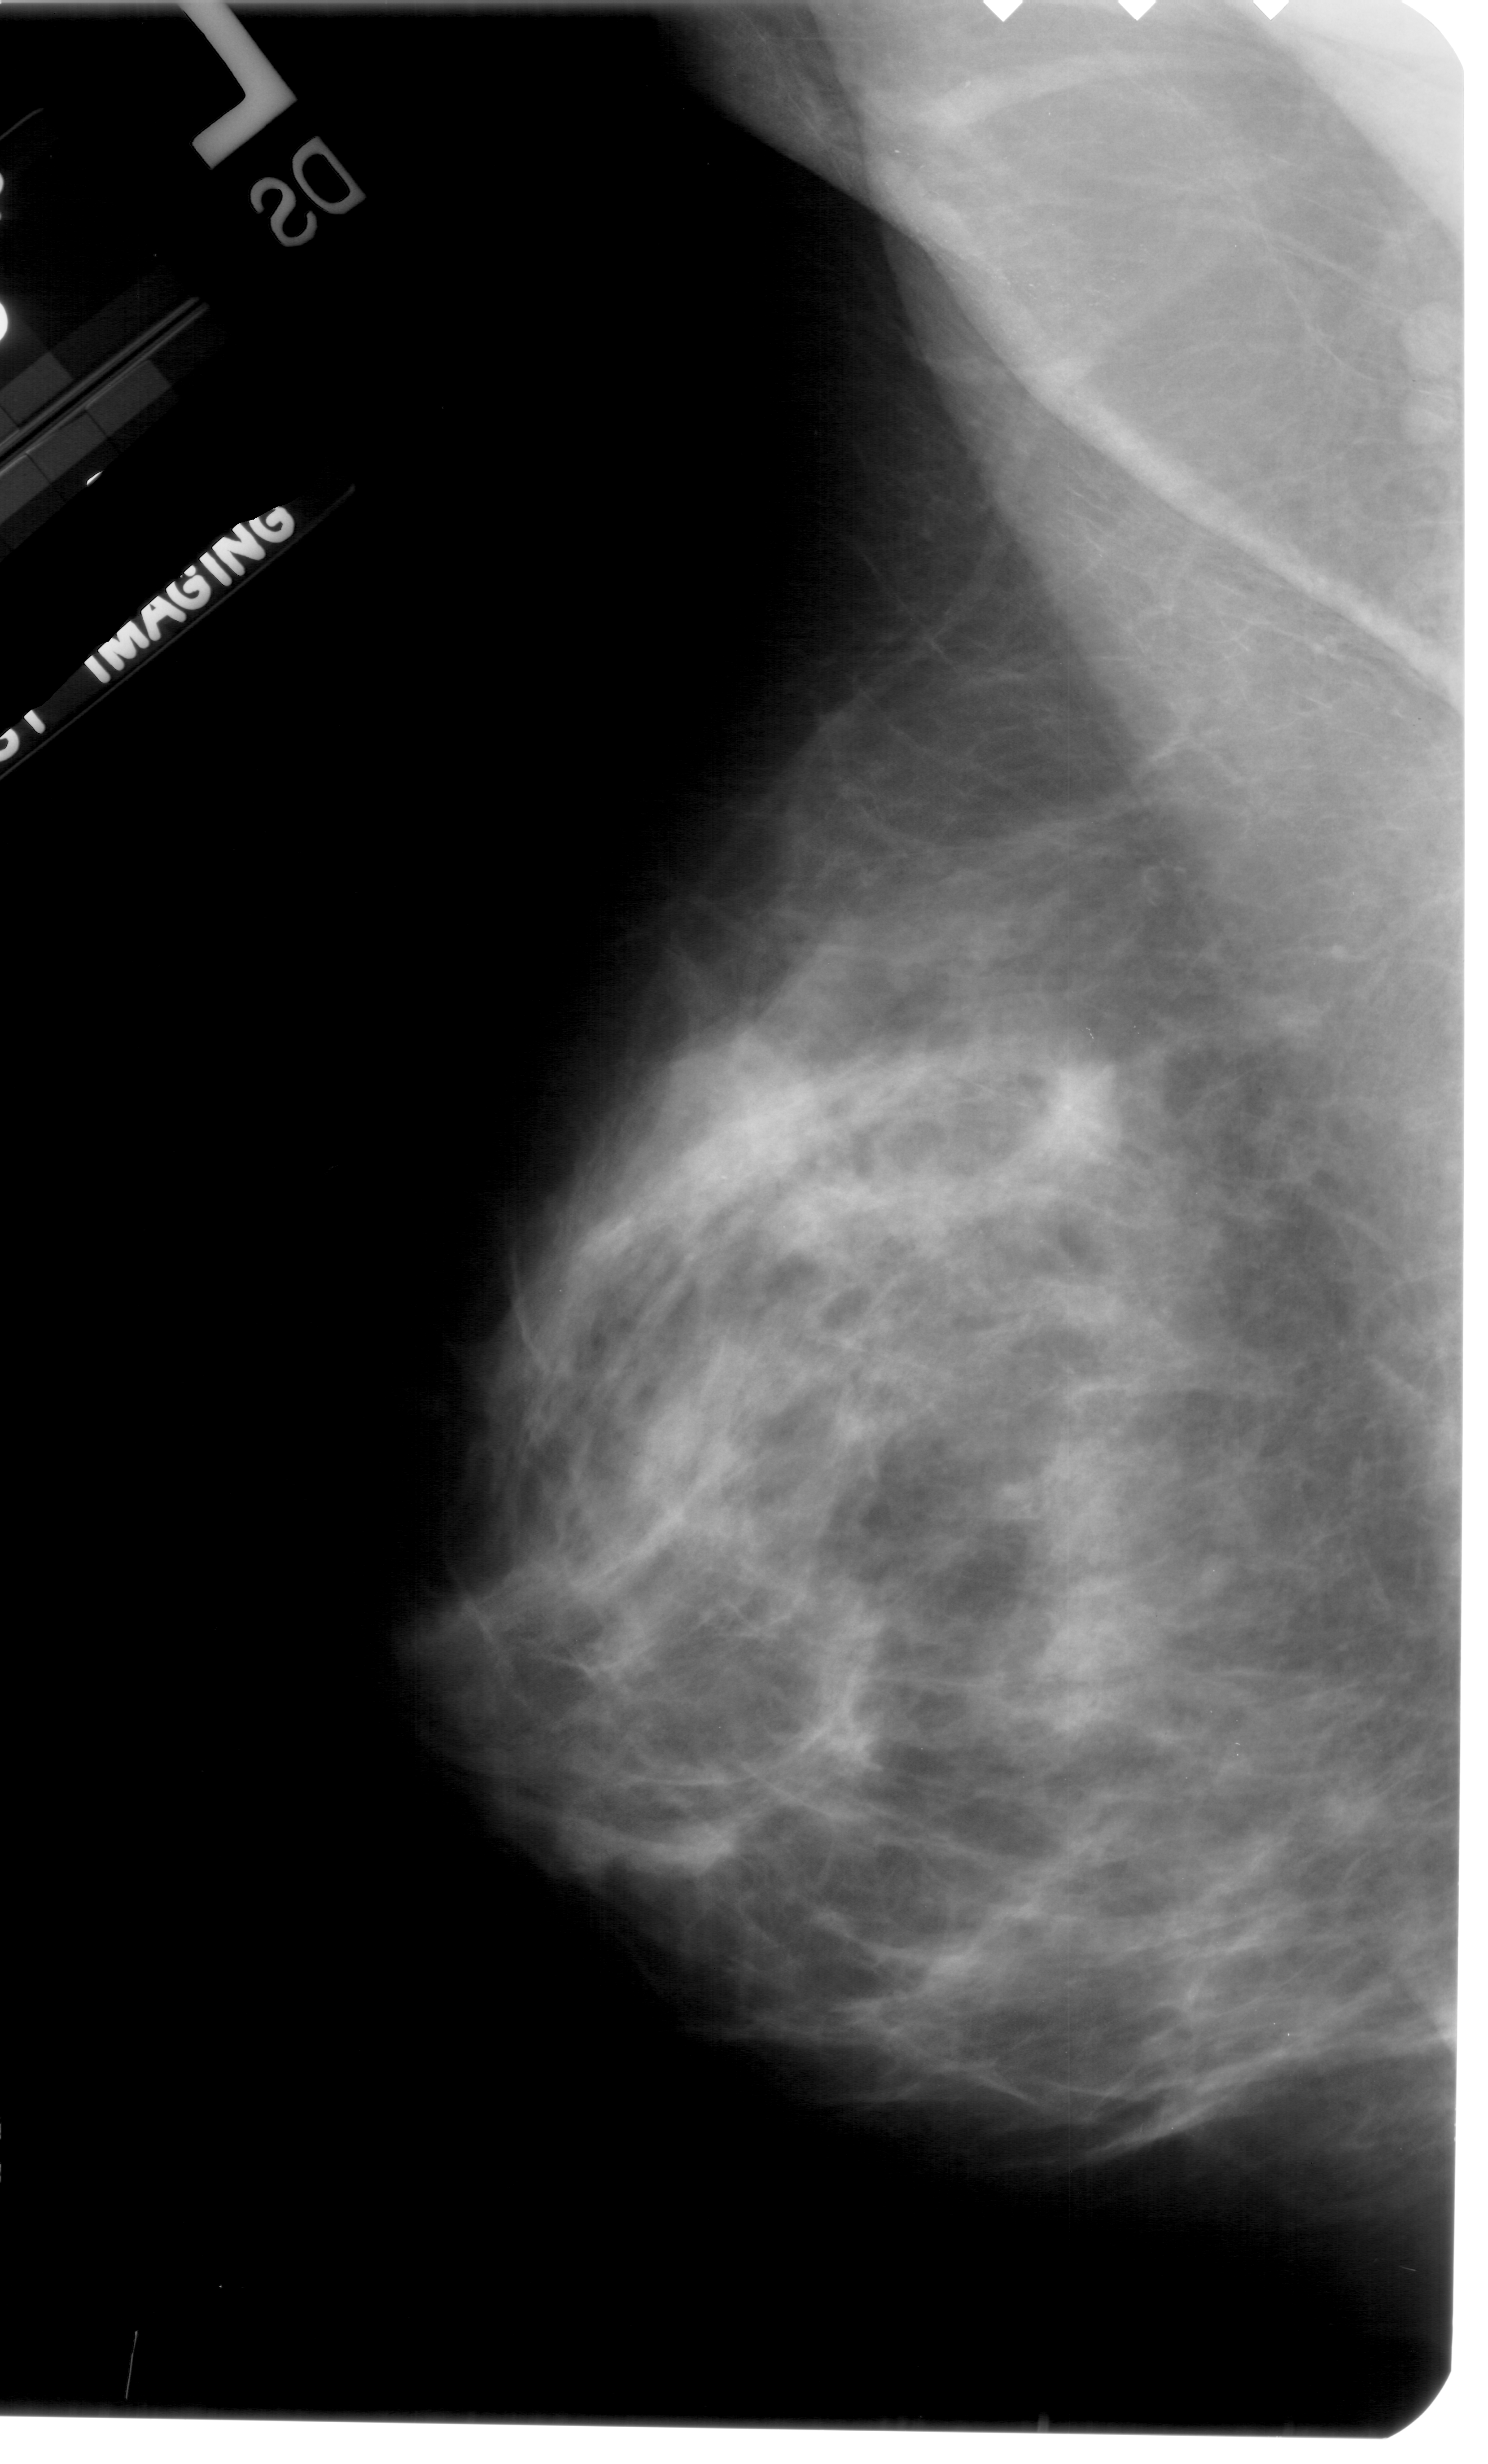
Mammogram (digitized film); left breast; mediolateral oblique (MLO) view; BI-RADS breast density category 4 (scale 1–4); 1488 × 2464 image matrix.
Marked abnormalities (boxes around the expert regions of interest):
- mass, shape focal asymmetric density, margins ill defined; BI-RADS assessment category 4; pathology result (as recorded, not read from the image): malignant: box from (x=1019, y=1064) to (x=1129, y=1173) px